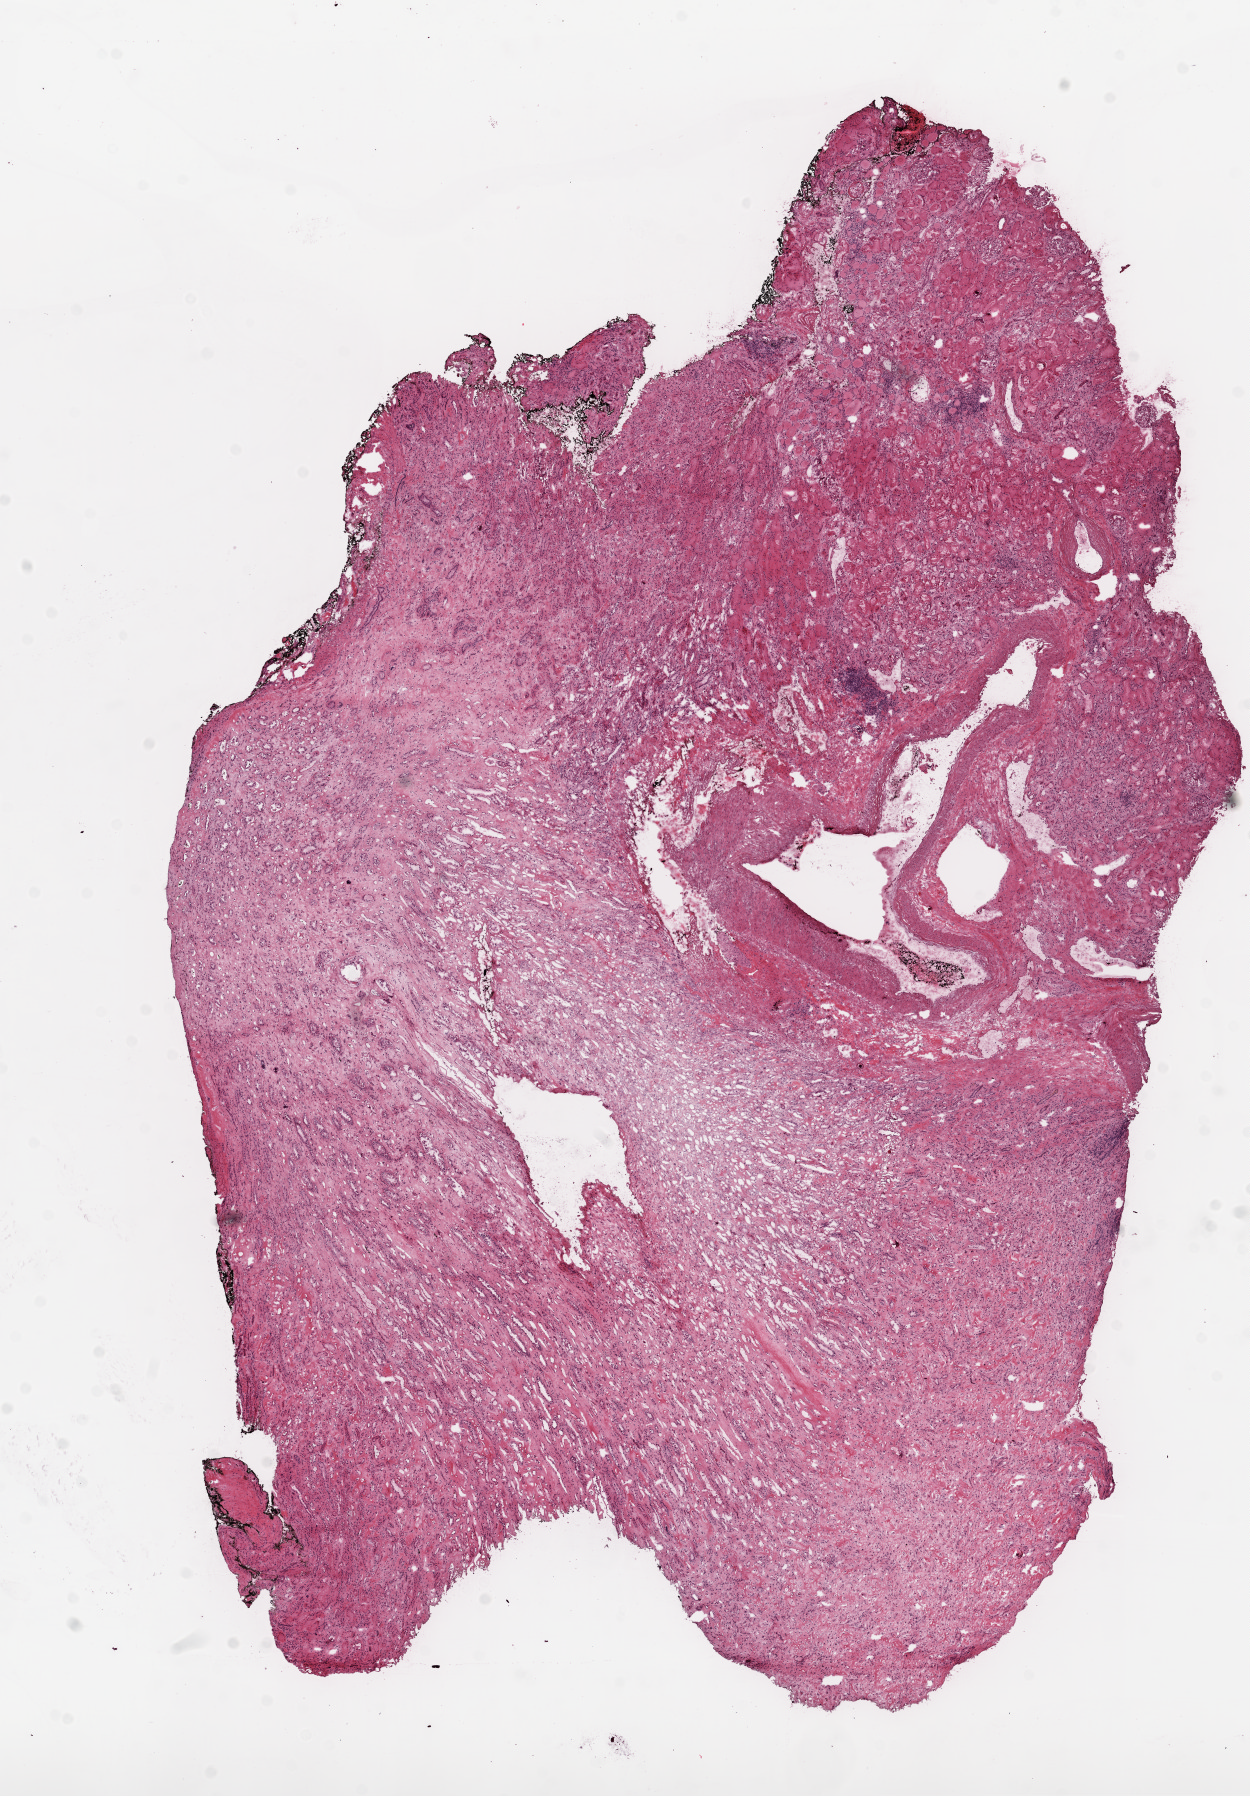
Whole-slide histology image, H&E-stained — shown as a low-resolution overview of the whole scanned area (about 10.0 x 14.4 mm). Frozen section. Sample: solid tissue normal (non-tumour tissue), kidney. Male patient; age at initial diagnosis 75 years.
This section: solid tissue normal sample (biorepository sample class). Patient diagnosis: Clear cell adenocarcinoma, NOS.